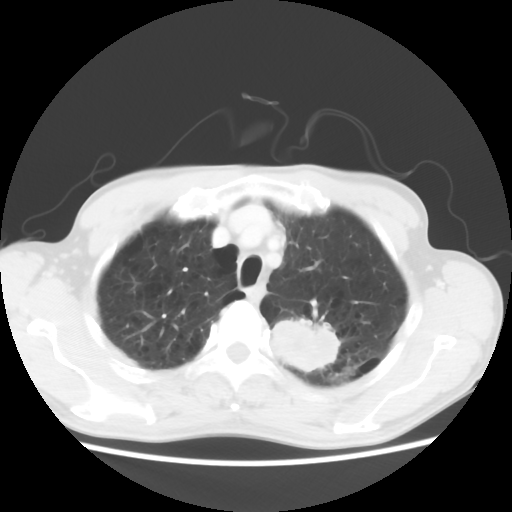
Chest CT, one axial slice; slice 52 of 64 in the series (ordered by position); 120 kVp; lung window (W 1500 / L -600 HU); 512 × 512 image matrix, field of view 346 × 346 mm. Patient: male, 63 years. From the clinical record (not read from this slice): clinical TNM (as recorded): T2 N0 M0.
Annotated regions visible in this slice (bounding box drawn by a radiologist):
- lung tumour (recorded histology: adenocarcinoma): bounding box (x1, y1, x2, y2) in pixels: (272, 309, 344, 382)